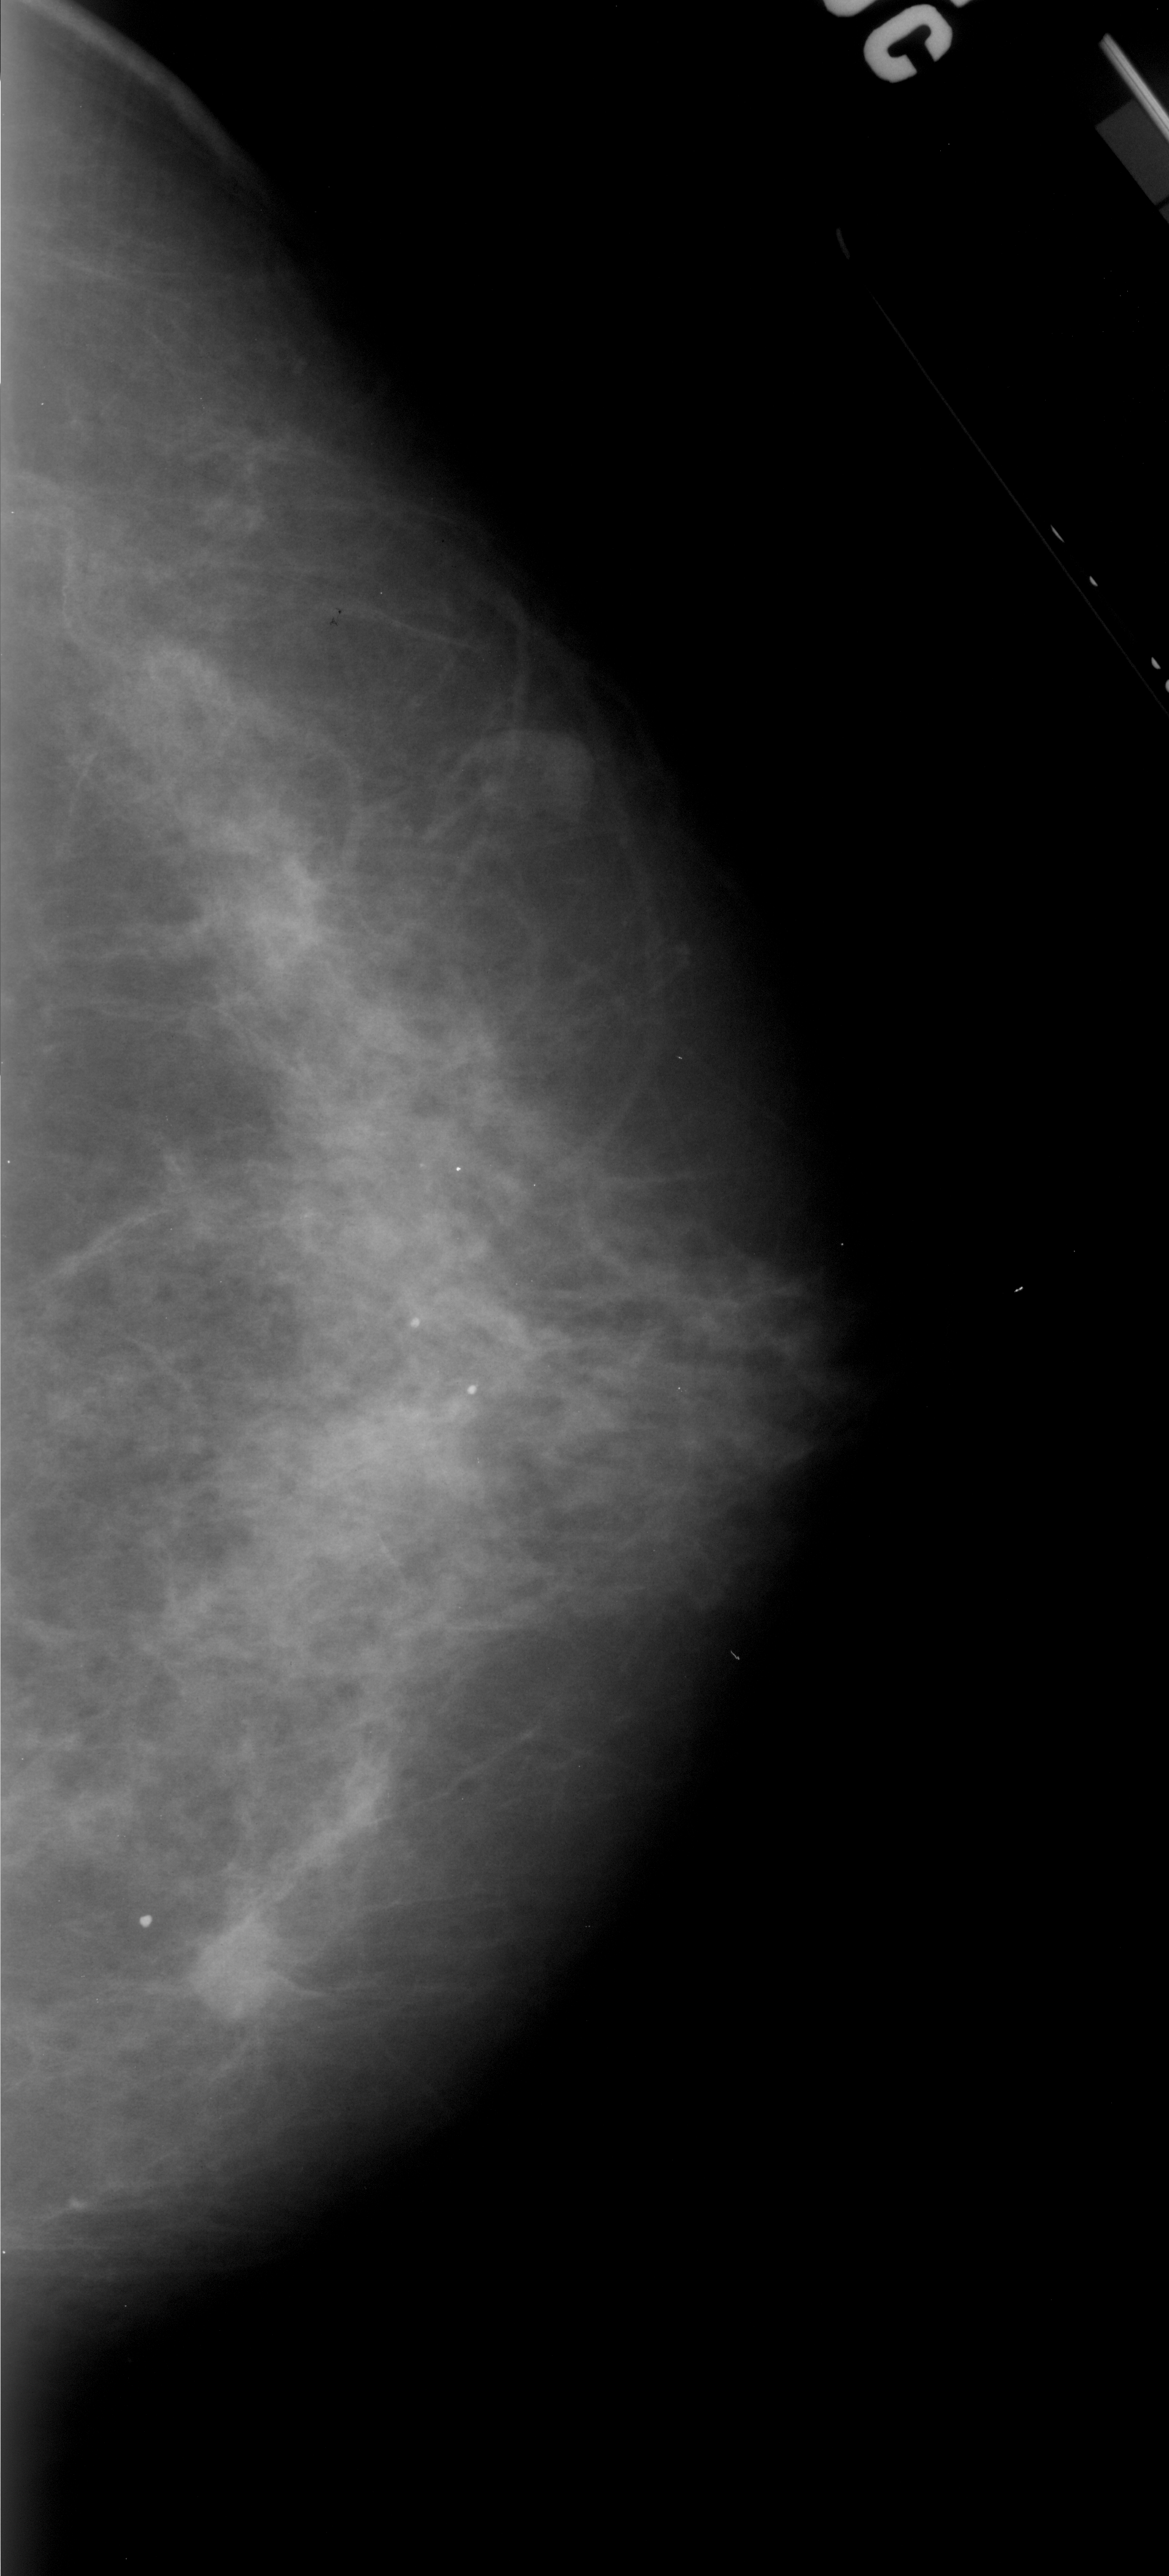
Scanned film-screen mammogram; right breast; craniocaudal (CC) view; BI-RADS breast density category 3 (scale 1–4); 1169 × 2576 image matrix.
Expert-marked regions of interest on this image (one box per marked abnormality):
- mass, shape lobulated, margins ill defined; BI-RADS assessment category 4; pathology (as recorded): malignant: bounding box <142,1870,312,2057> (left, top, right, bottom; pixels)